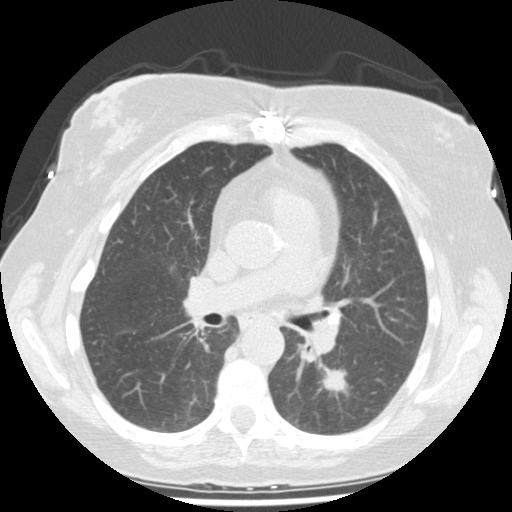
Low-dose screening chest CT, one axial slice; position 97 of 159 along the scan axis; 120 kVp; lung window (W 1500 / L -600 HU); 2.5 mm slice thickness; 512 × 512 image matrix, field of view 326 × 326 mm.
Outlined on this slice (expert manual segmentation):
- lesion 1 (tumor, lower lobe of left lung): bounding box <323,370,349,394> (left, top, right, bottom; pixels)